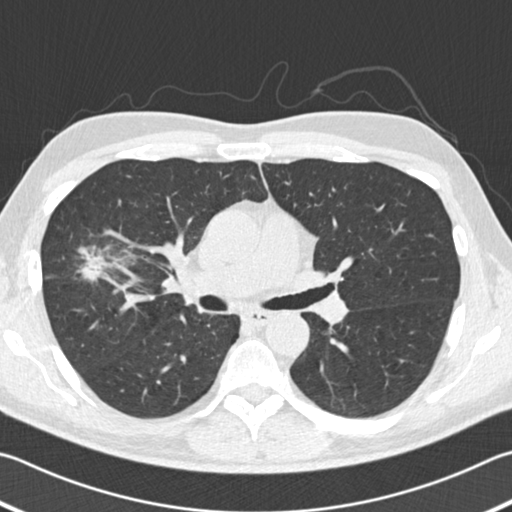
Low-dose screening chest CT, one axial slice. Reconstruction kernel B30f. Lung window (W 1500 / L -600 HU). 512 × 512 image matrix, field of view 344 × 344 mm.
Annotated regions visible in this slice (outlined manually by an expert reader):
- lesion 1 (tumor, upper lobe of right lung): bounding box (x1, y1, x2, y2) in pixels: (77, 246, 126, 280)